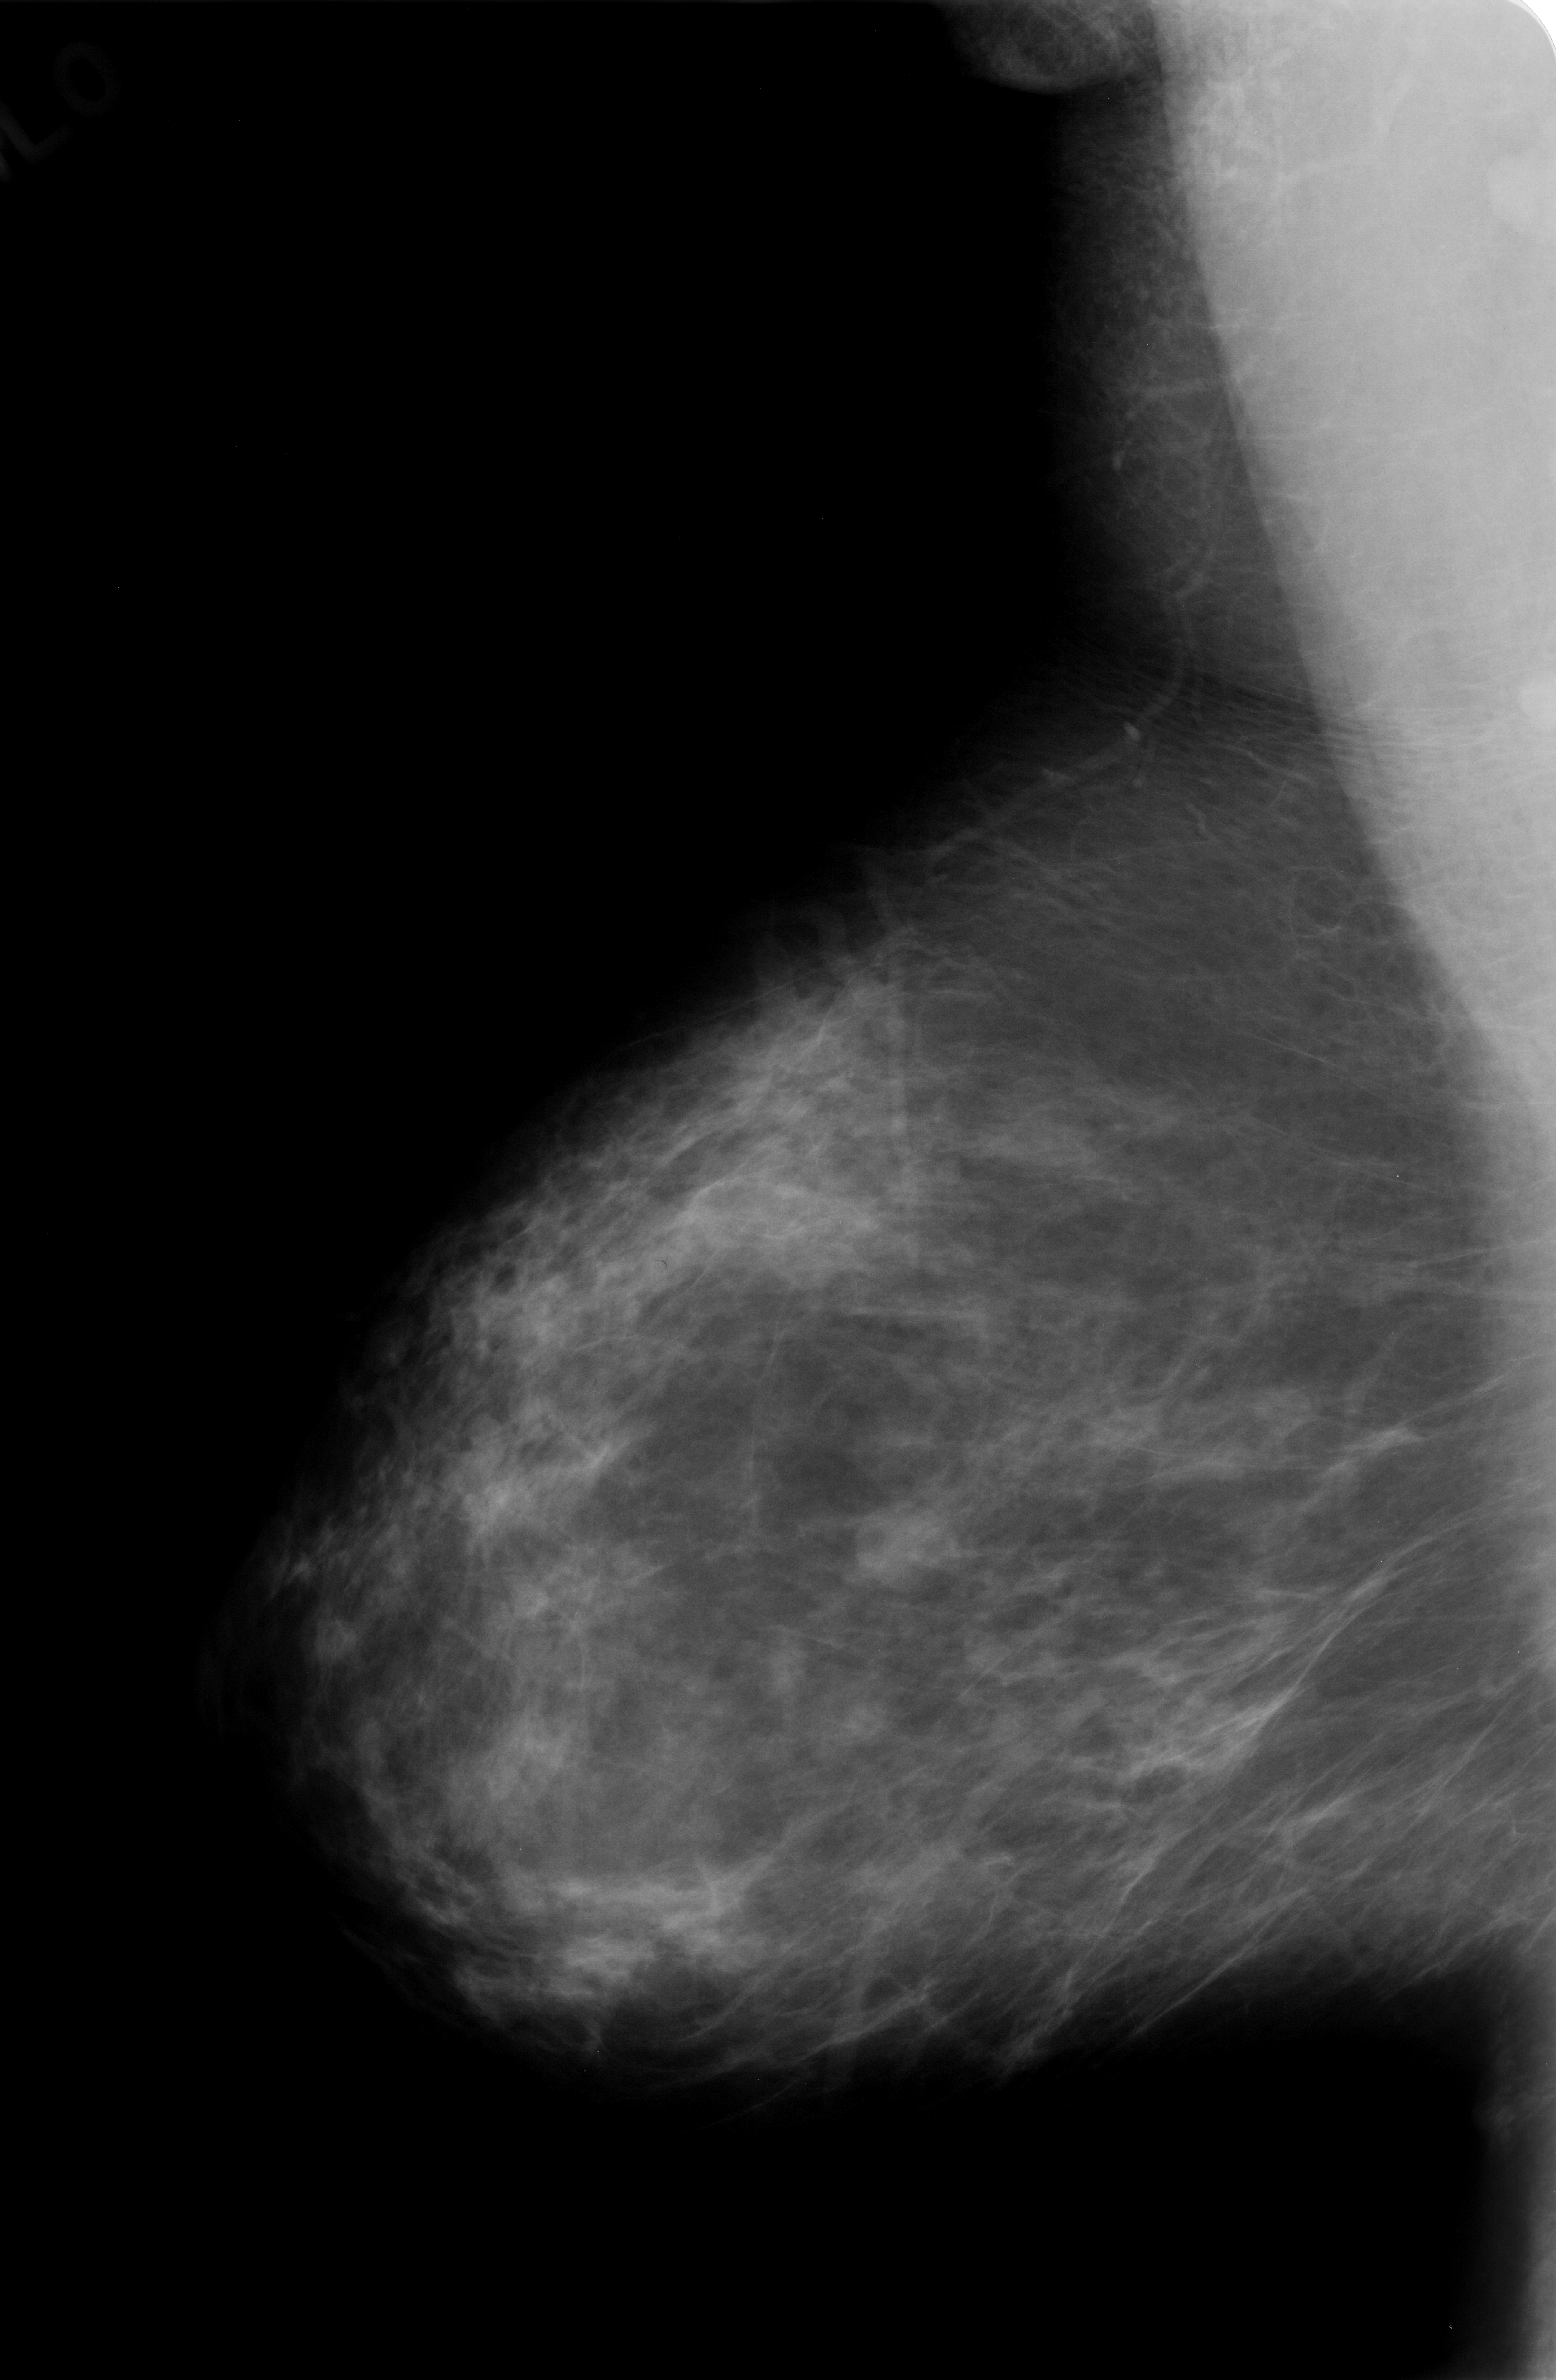
Digitized screen-film mammogram; right breast; MLO view; 1556 × 2380 image matrix.
Expert-marked regions of interest on this image (one box per marked abnormality):
- mass, shape oval, margins circumscribed; BI-RADS assessment category 3; subtlety rating 4 on a 1 (subtle) to 5 (obvious) scale; pathology (as recorded): benign: bounding box (x1, y1, x2, y2) in pixels: (860, 1506, 970, 1586)